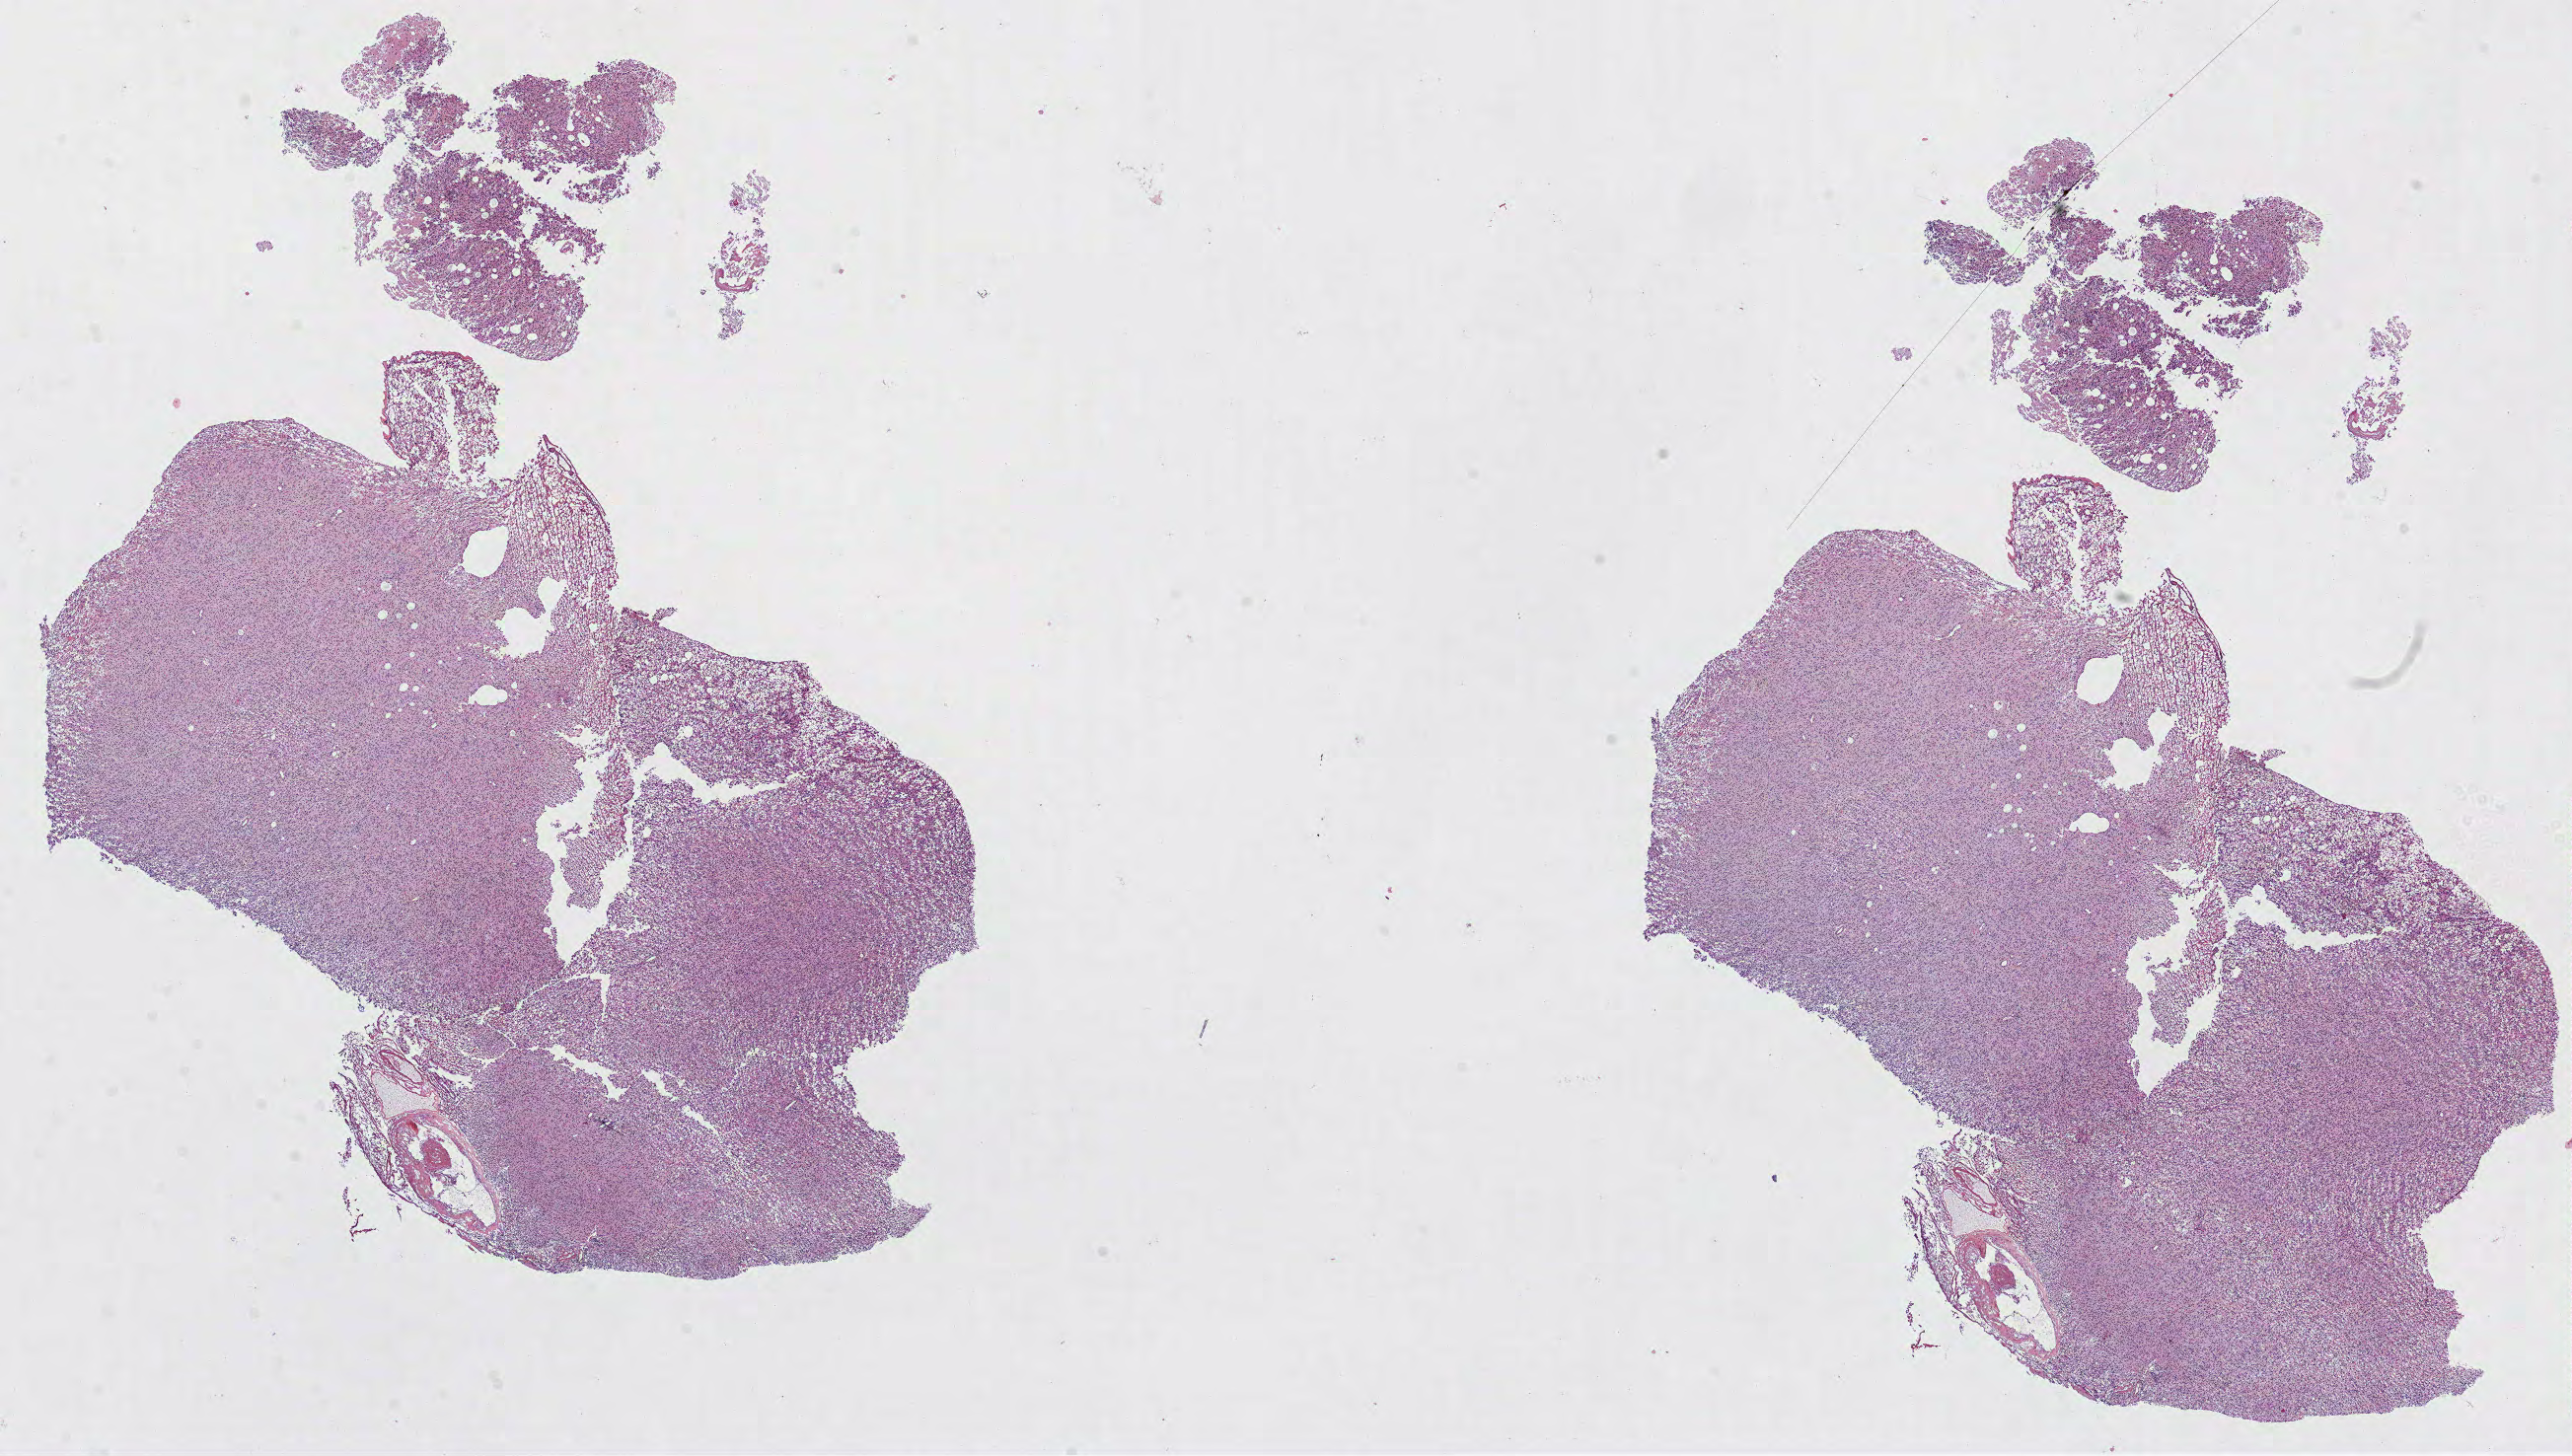
Hematoxylin and eosin (H&E) stained whole-slide image, a low-resolution overview of the entire scanned area, about 21.0 x 11.9 mm; formalin-fixed paraffin-embedded (FFPE) diagnostic section; sample: primary tumour, brain. Patient: male, age at initial diagnosis 60 years.
Diagnosis: Glioblastoma.